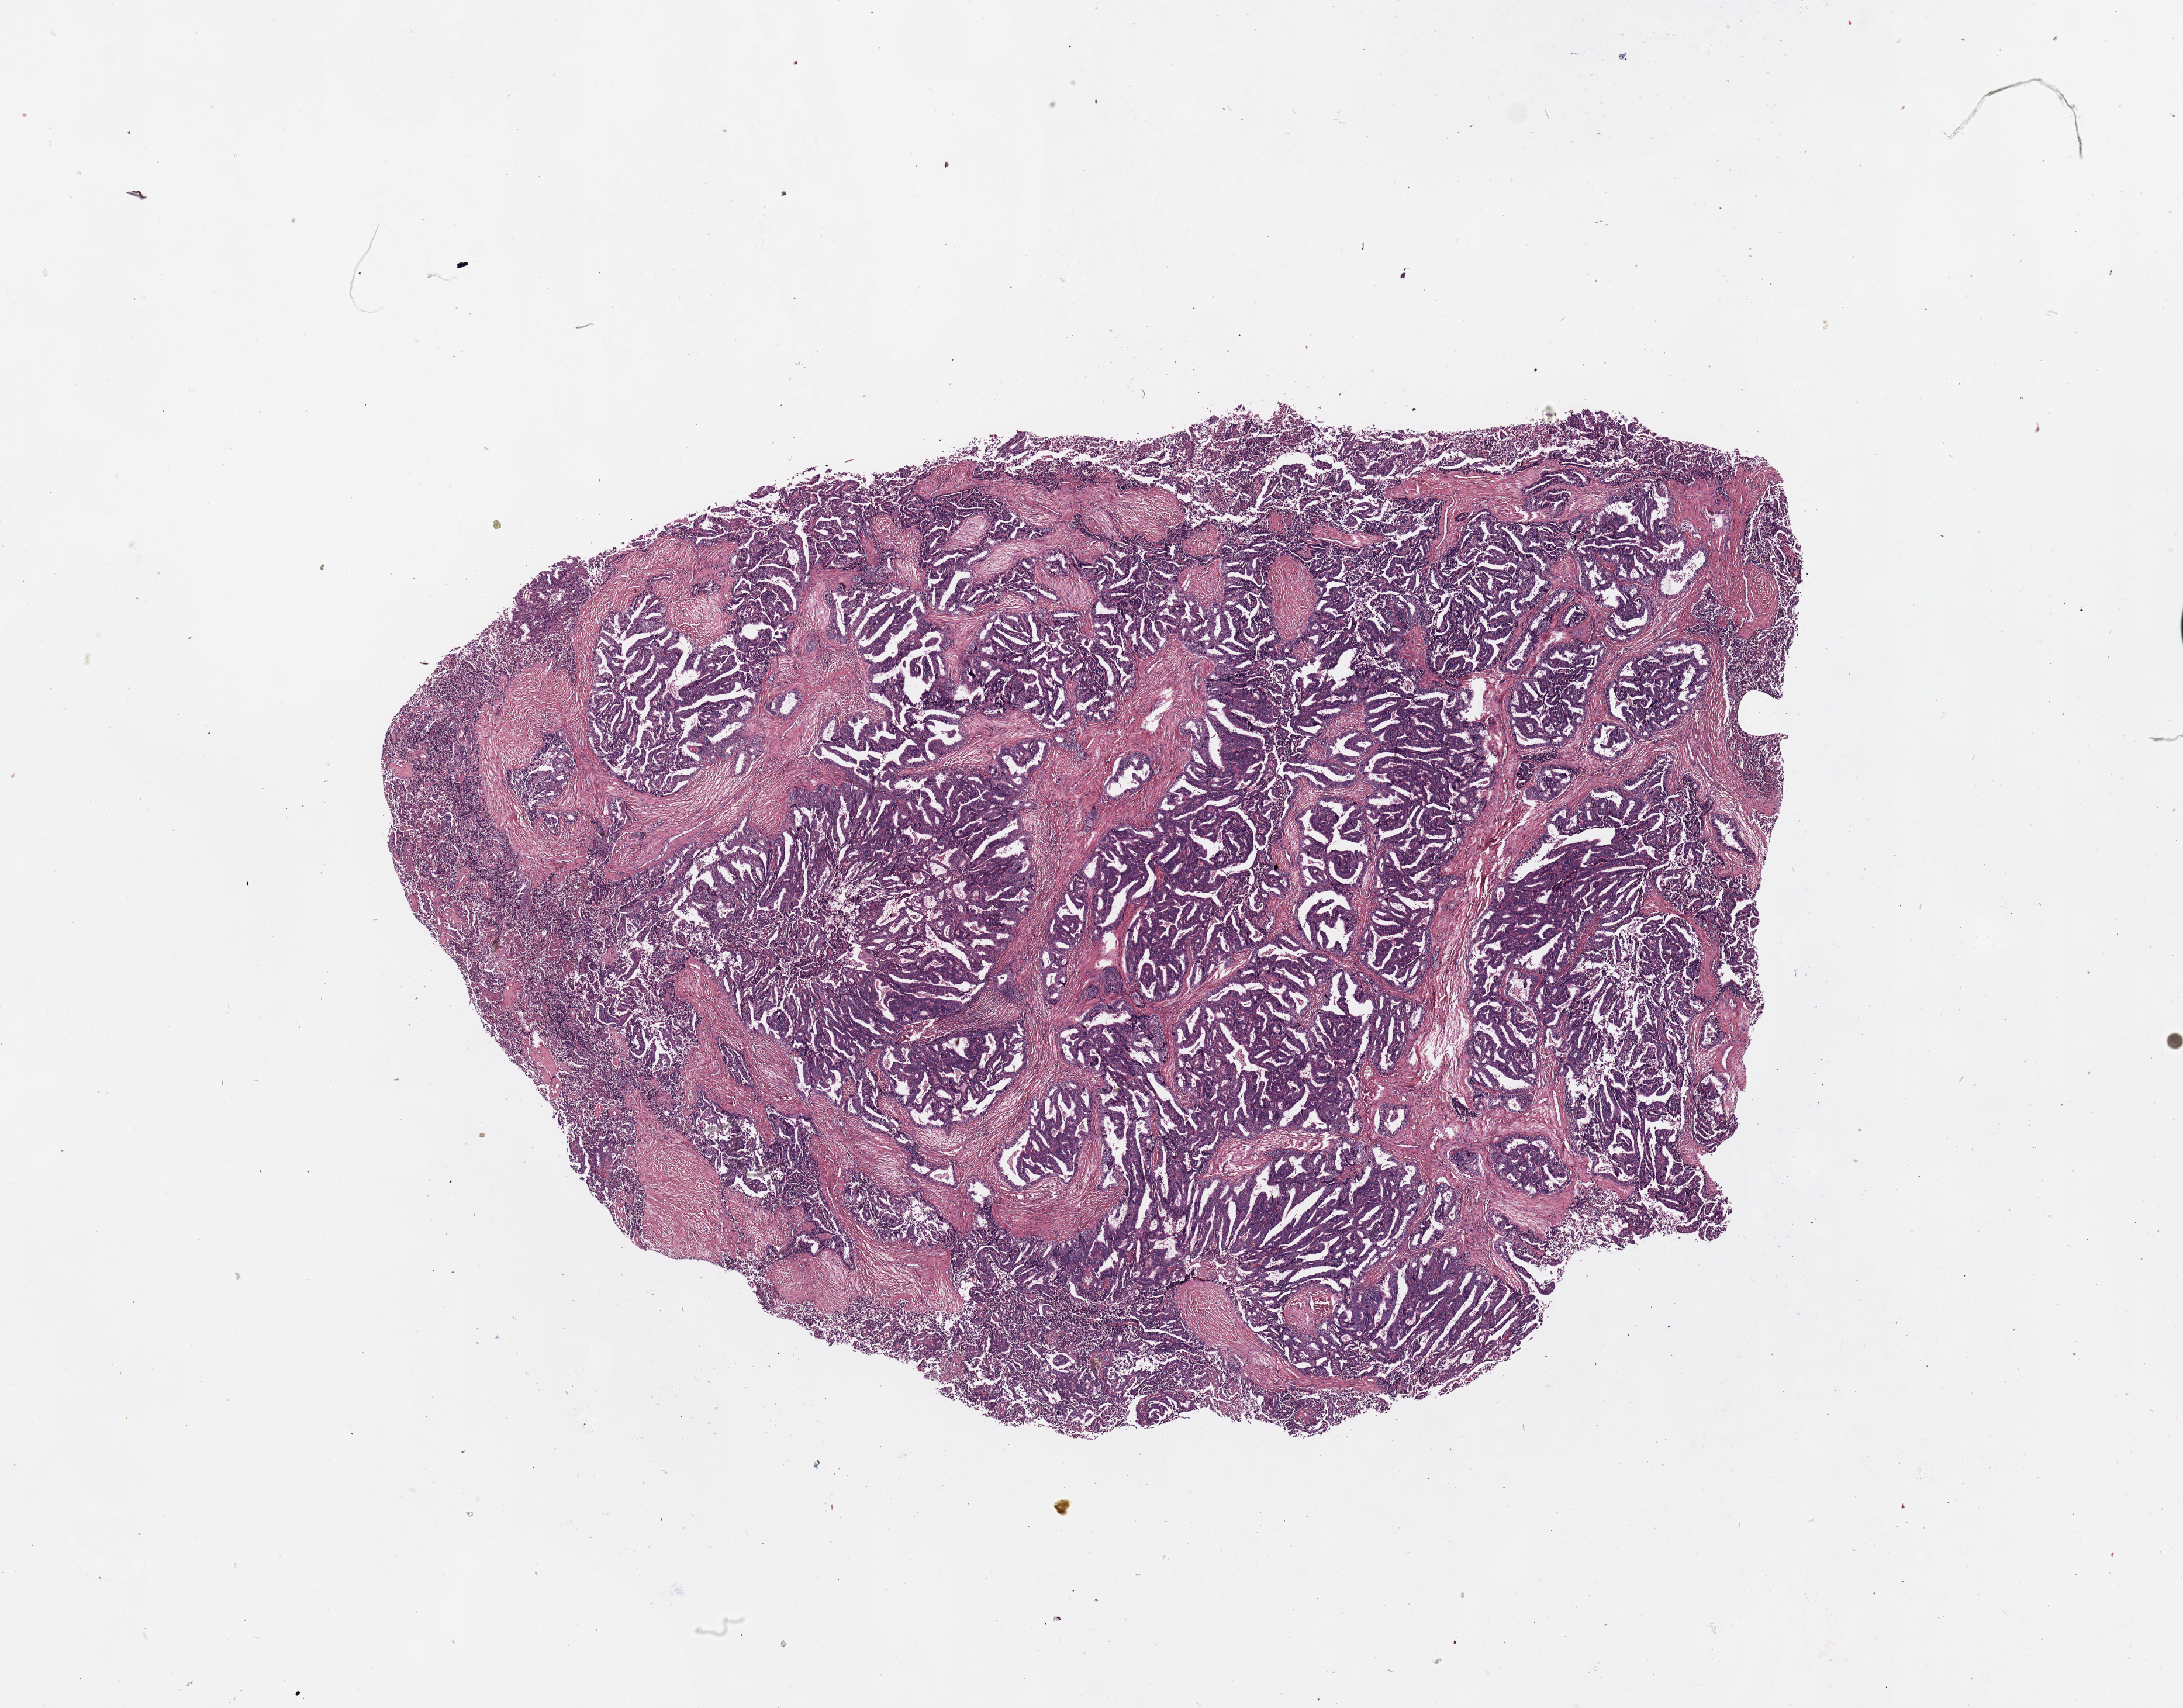
Whole-slide histology image, Hematoxylin and eosin (H&E) stained, a low-resolution overview of the entire scanned area, about 14.8 x 11.6 mm (acquisition: 20x scan); uterus, tumour tissue. 57-year-old female patient. Histologic grade: G2 (moderately differentiated).
Histologic diagnosis: Endometrioid adenocarcinoma, NOS. AJCC pathologic stage: III.